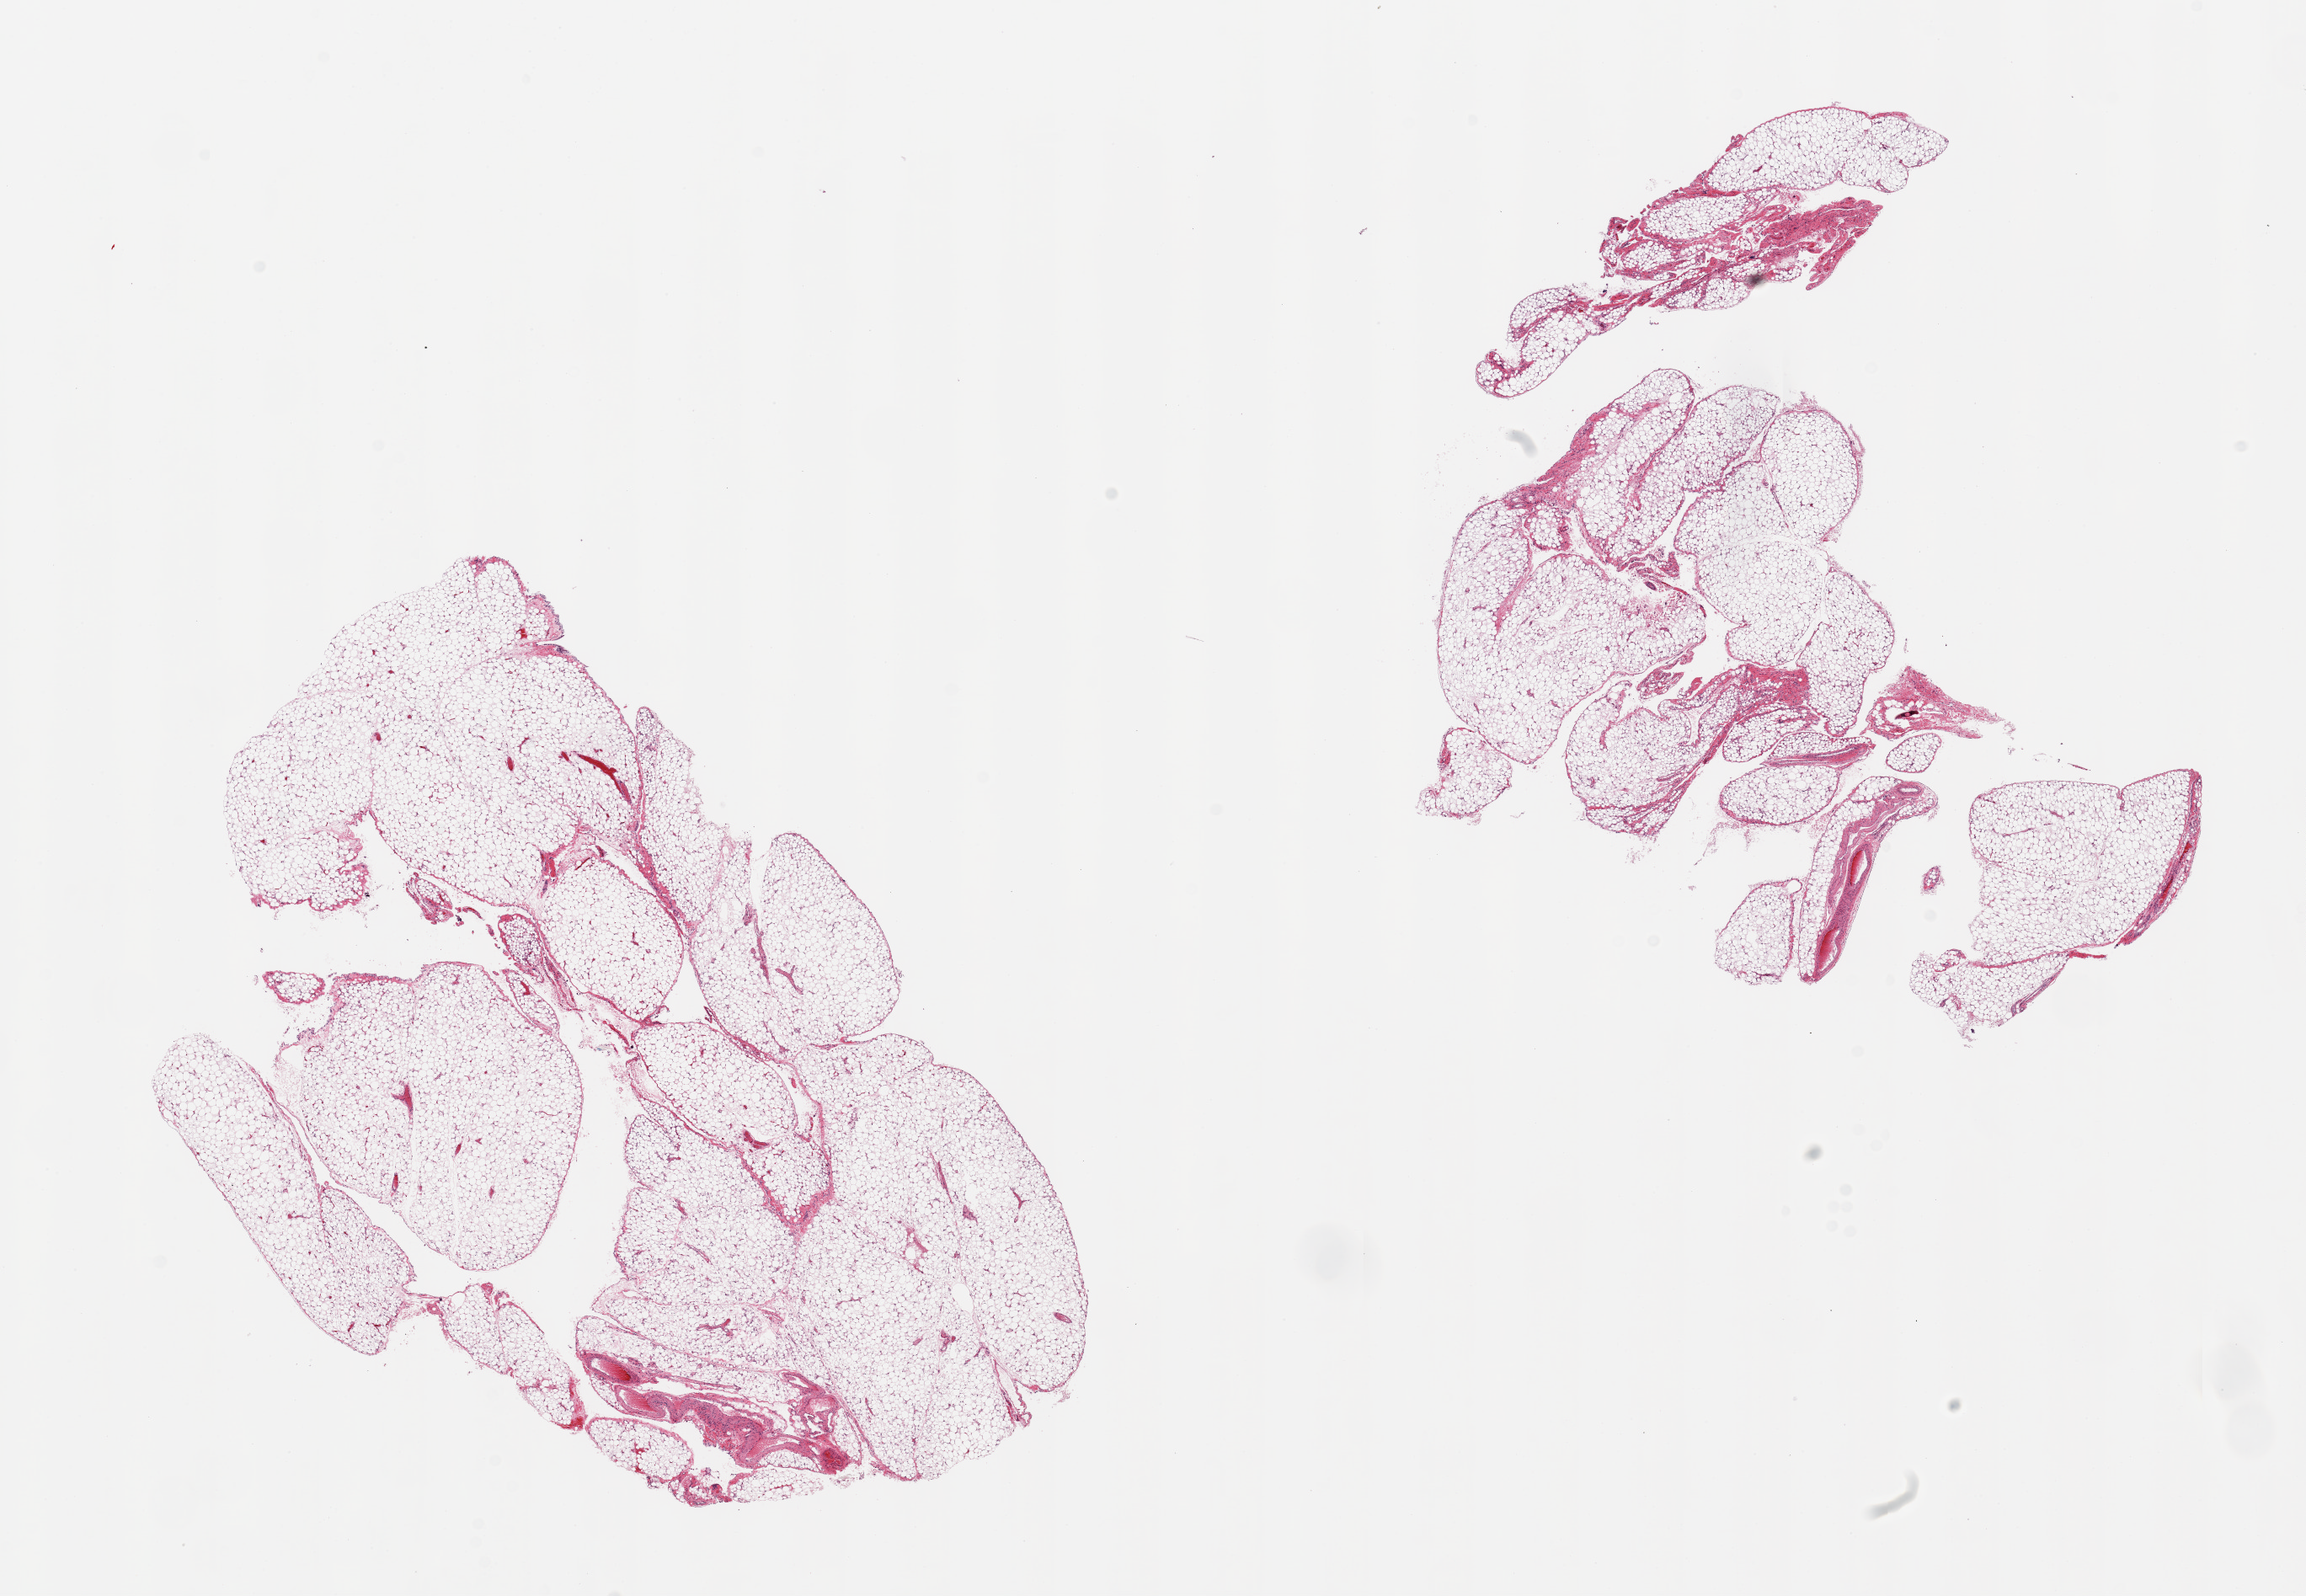
Whole-slide image, hematoxylin and eosin (H&E) stain, brightfield, a low-resolution overview of the entire scanned area, about 21.7 x 15.0 mm (slide scanned at 20x). PAXgene-fixed paraffin-embedded (PFPE) section. Target tissue: omentum. Donor tissue sample. Donor sex: female.
- review note (as recorded): 2 pieces